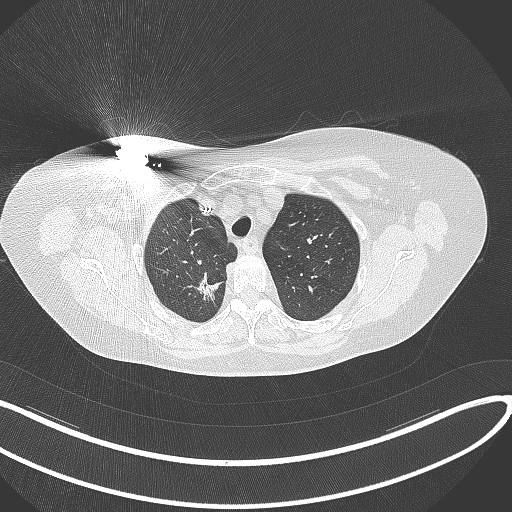
Chest CT, one axial slice. Position 272 of 316 along the scan axis. Reconstruction kernel B70f. 120 kVp. Lung window (W 1500 / L -600 HU). 1 mm slice thickness. 512 × 512 image matrix, field of view 400 × 400 mm. Patient: female, 72 years. From the clinical record (not read from this slice): clinical TNM (as recorded): T1c N0 M0.
Structures marked on this image (rectangle marked by the reading radiologist):
- lung tumour (recorded histology: adenocarcinoma): bounding box (x1, y1, x2, y2) in pixels: (193, 269, 225, 305)